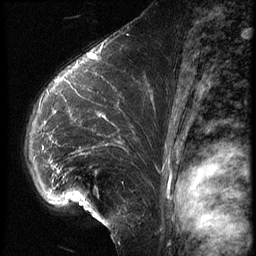
Breast MRI (dynamic contrast-enhanced), one sagittal slice; slice 40 of 62 in the series (ordered by position); 3 images stored at this slice position (order not interpretable as contrast timing); 1.5 T; TE 4.2 ms, TR 9 ms; 2.5 mm slice thickness; 256 × 256 image matrix. Female patient, age 39 years. From the clinical record (not read from this slice): setting: breast cancer imaged before/during neoadjuvant chemotherapy; receptor status: HER2-positive.
Outlined on this slice (semi-automatically segmented with operator editing):
- analysis volume of interest (the breast-tissue region the enhancement analysis was run in; not a lesion): box from (x=22, y=64) to (x=156, y=228) px
- tumour enhancement mask (voxels above the 140 % enhancement threshold inside the analysis volume of interest): (x=43, y=82)–(x=101, y=184)